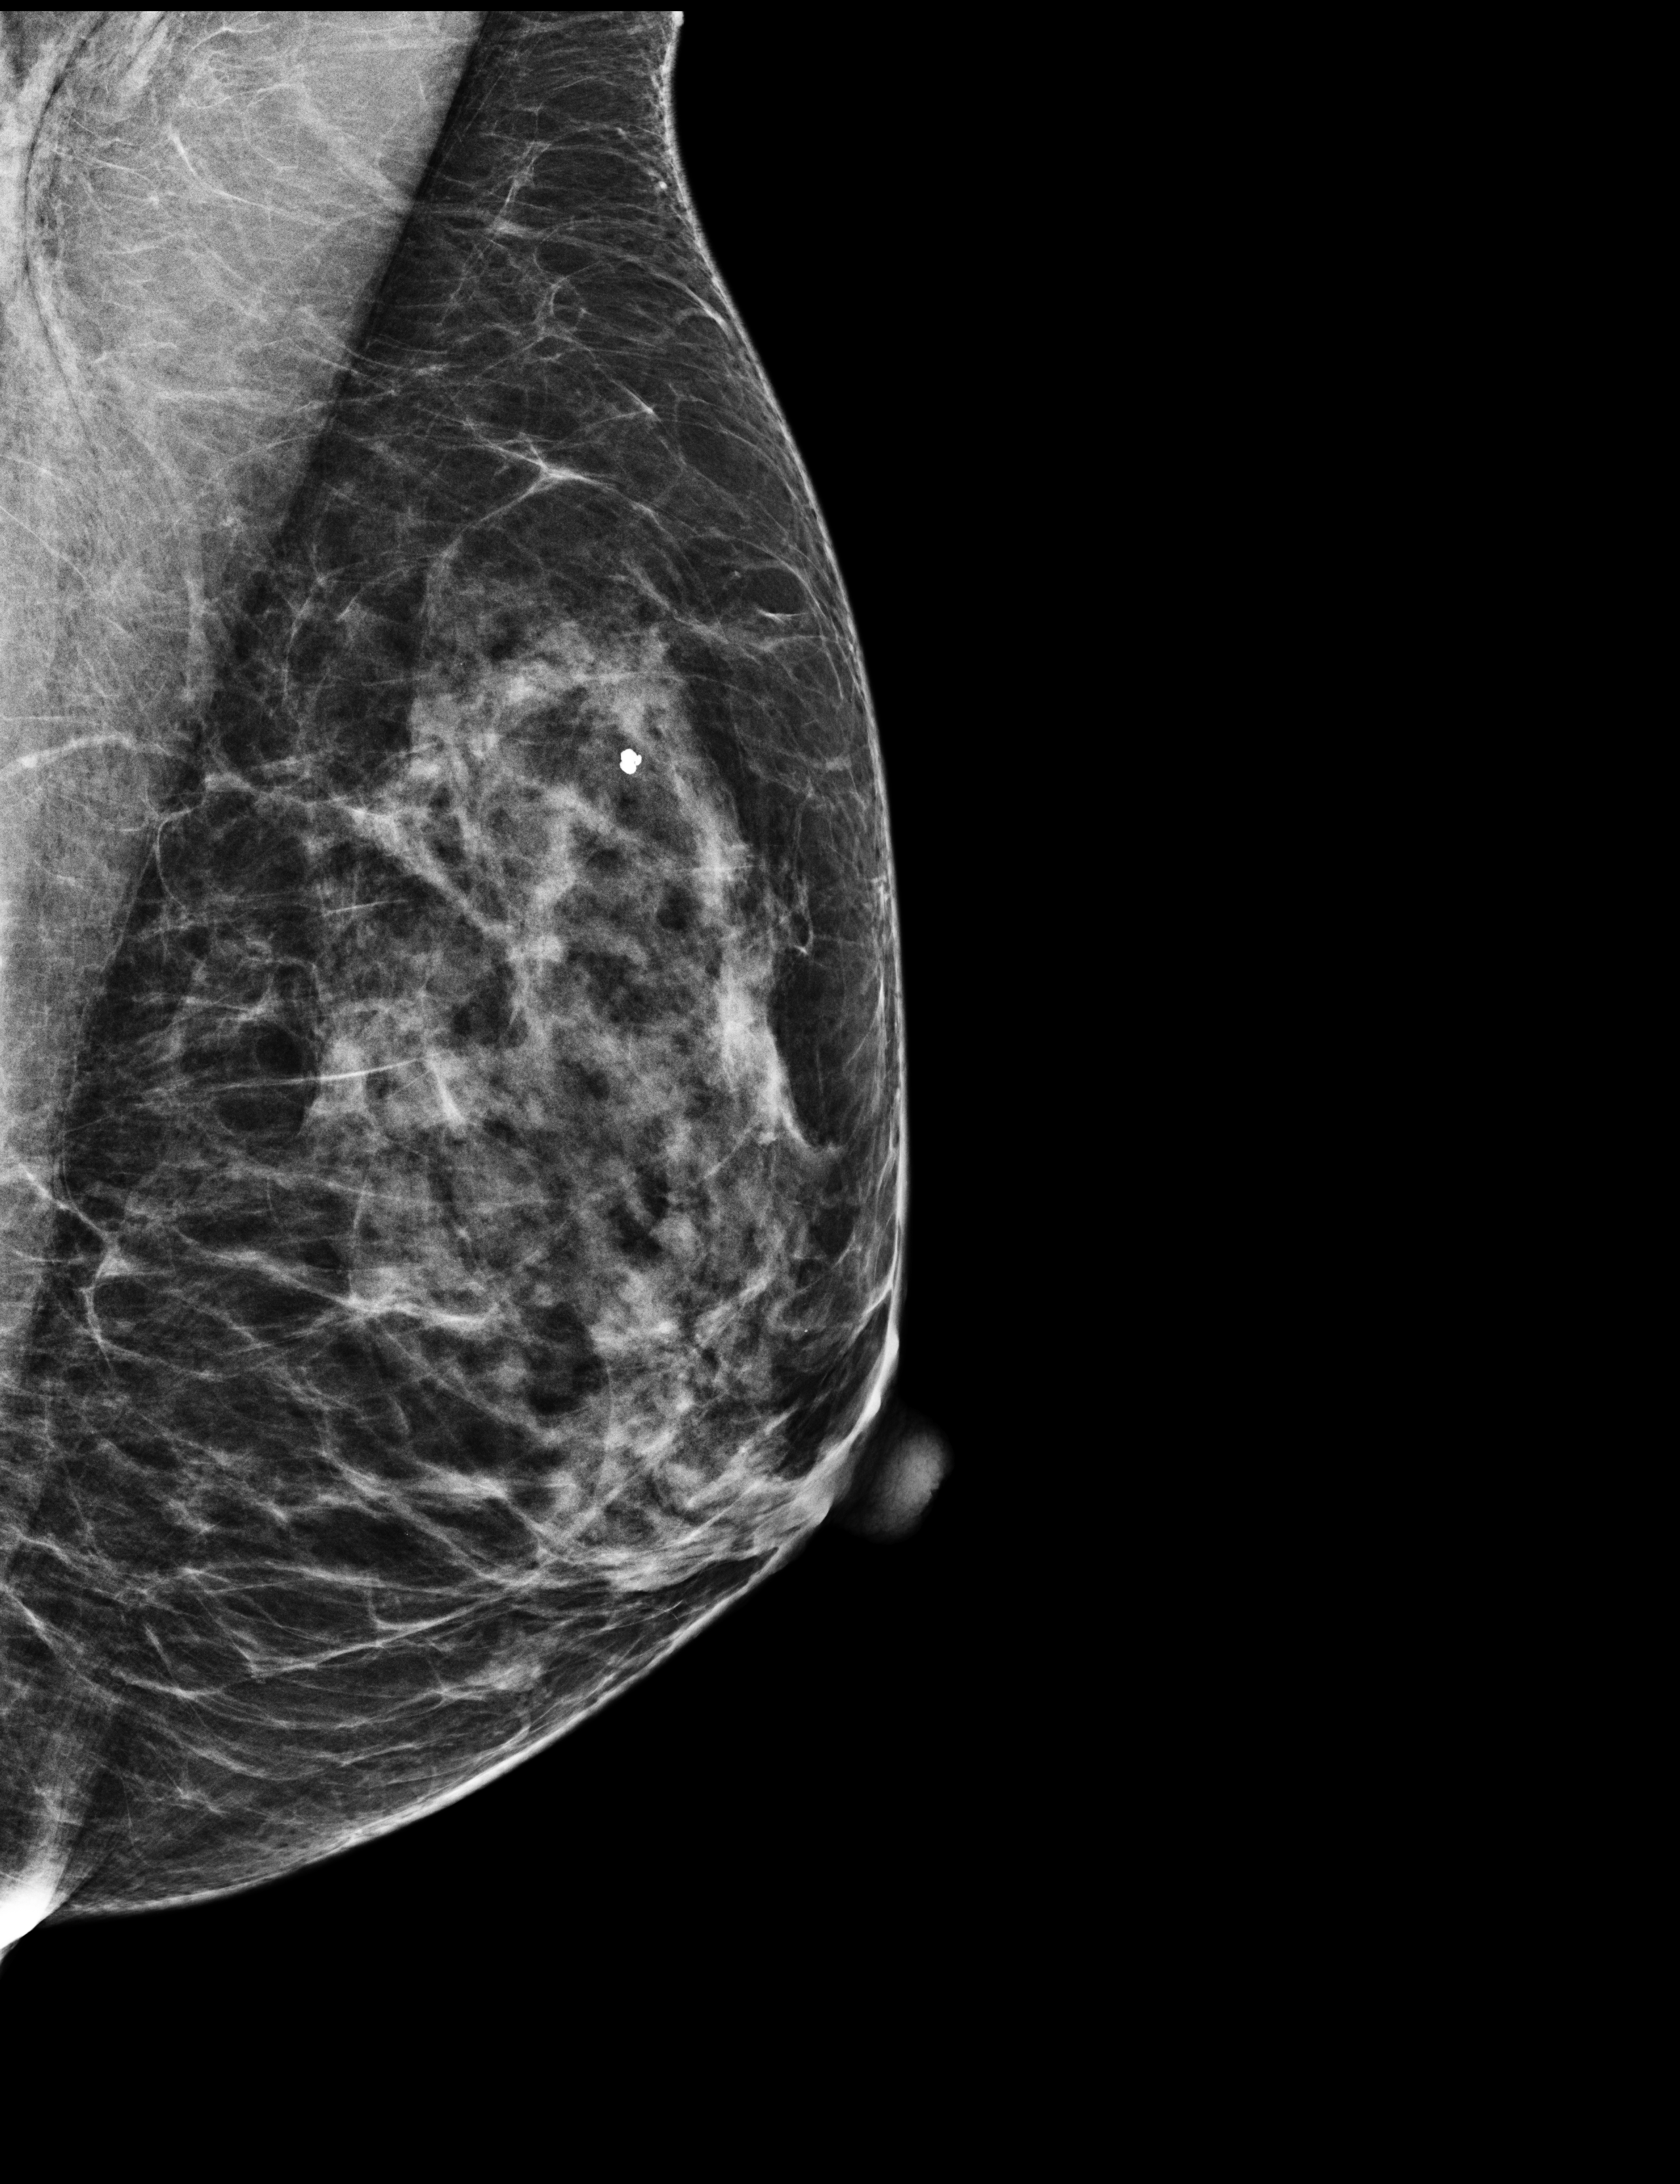
Full-field digital mammogram (FFDM), left breast, mediolateral oblique (MLO) view, screening examination. Patient: female, 60 years.
- breast density at the screening exam (both breasts): heterogeneously dense (BI-RADS density category c)
- final BI-RADS assessment for this screening round (tomosynthesis exam, both breasts): category 1
- recall: recalled for additional imaging after this screen